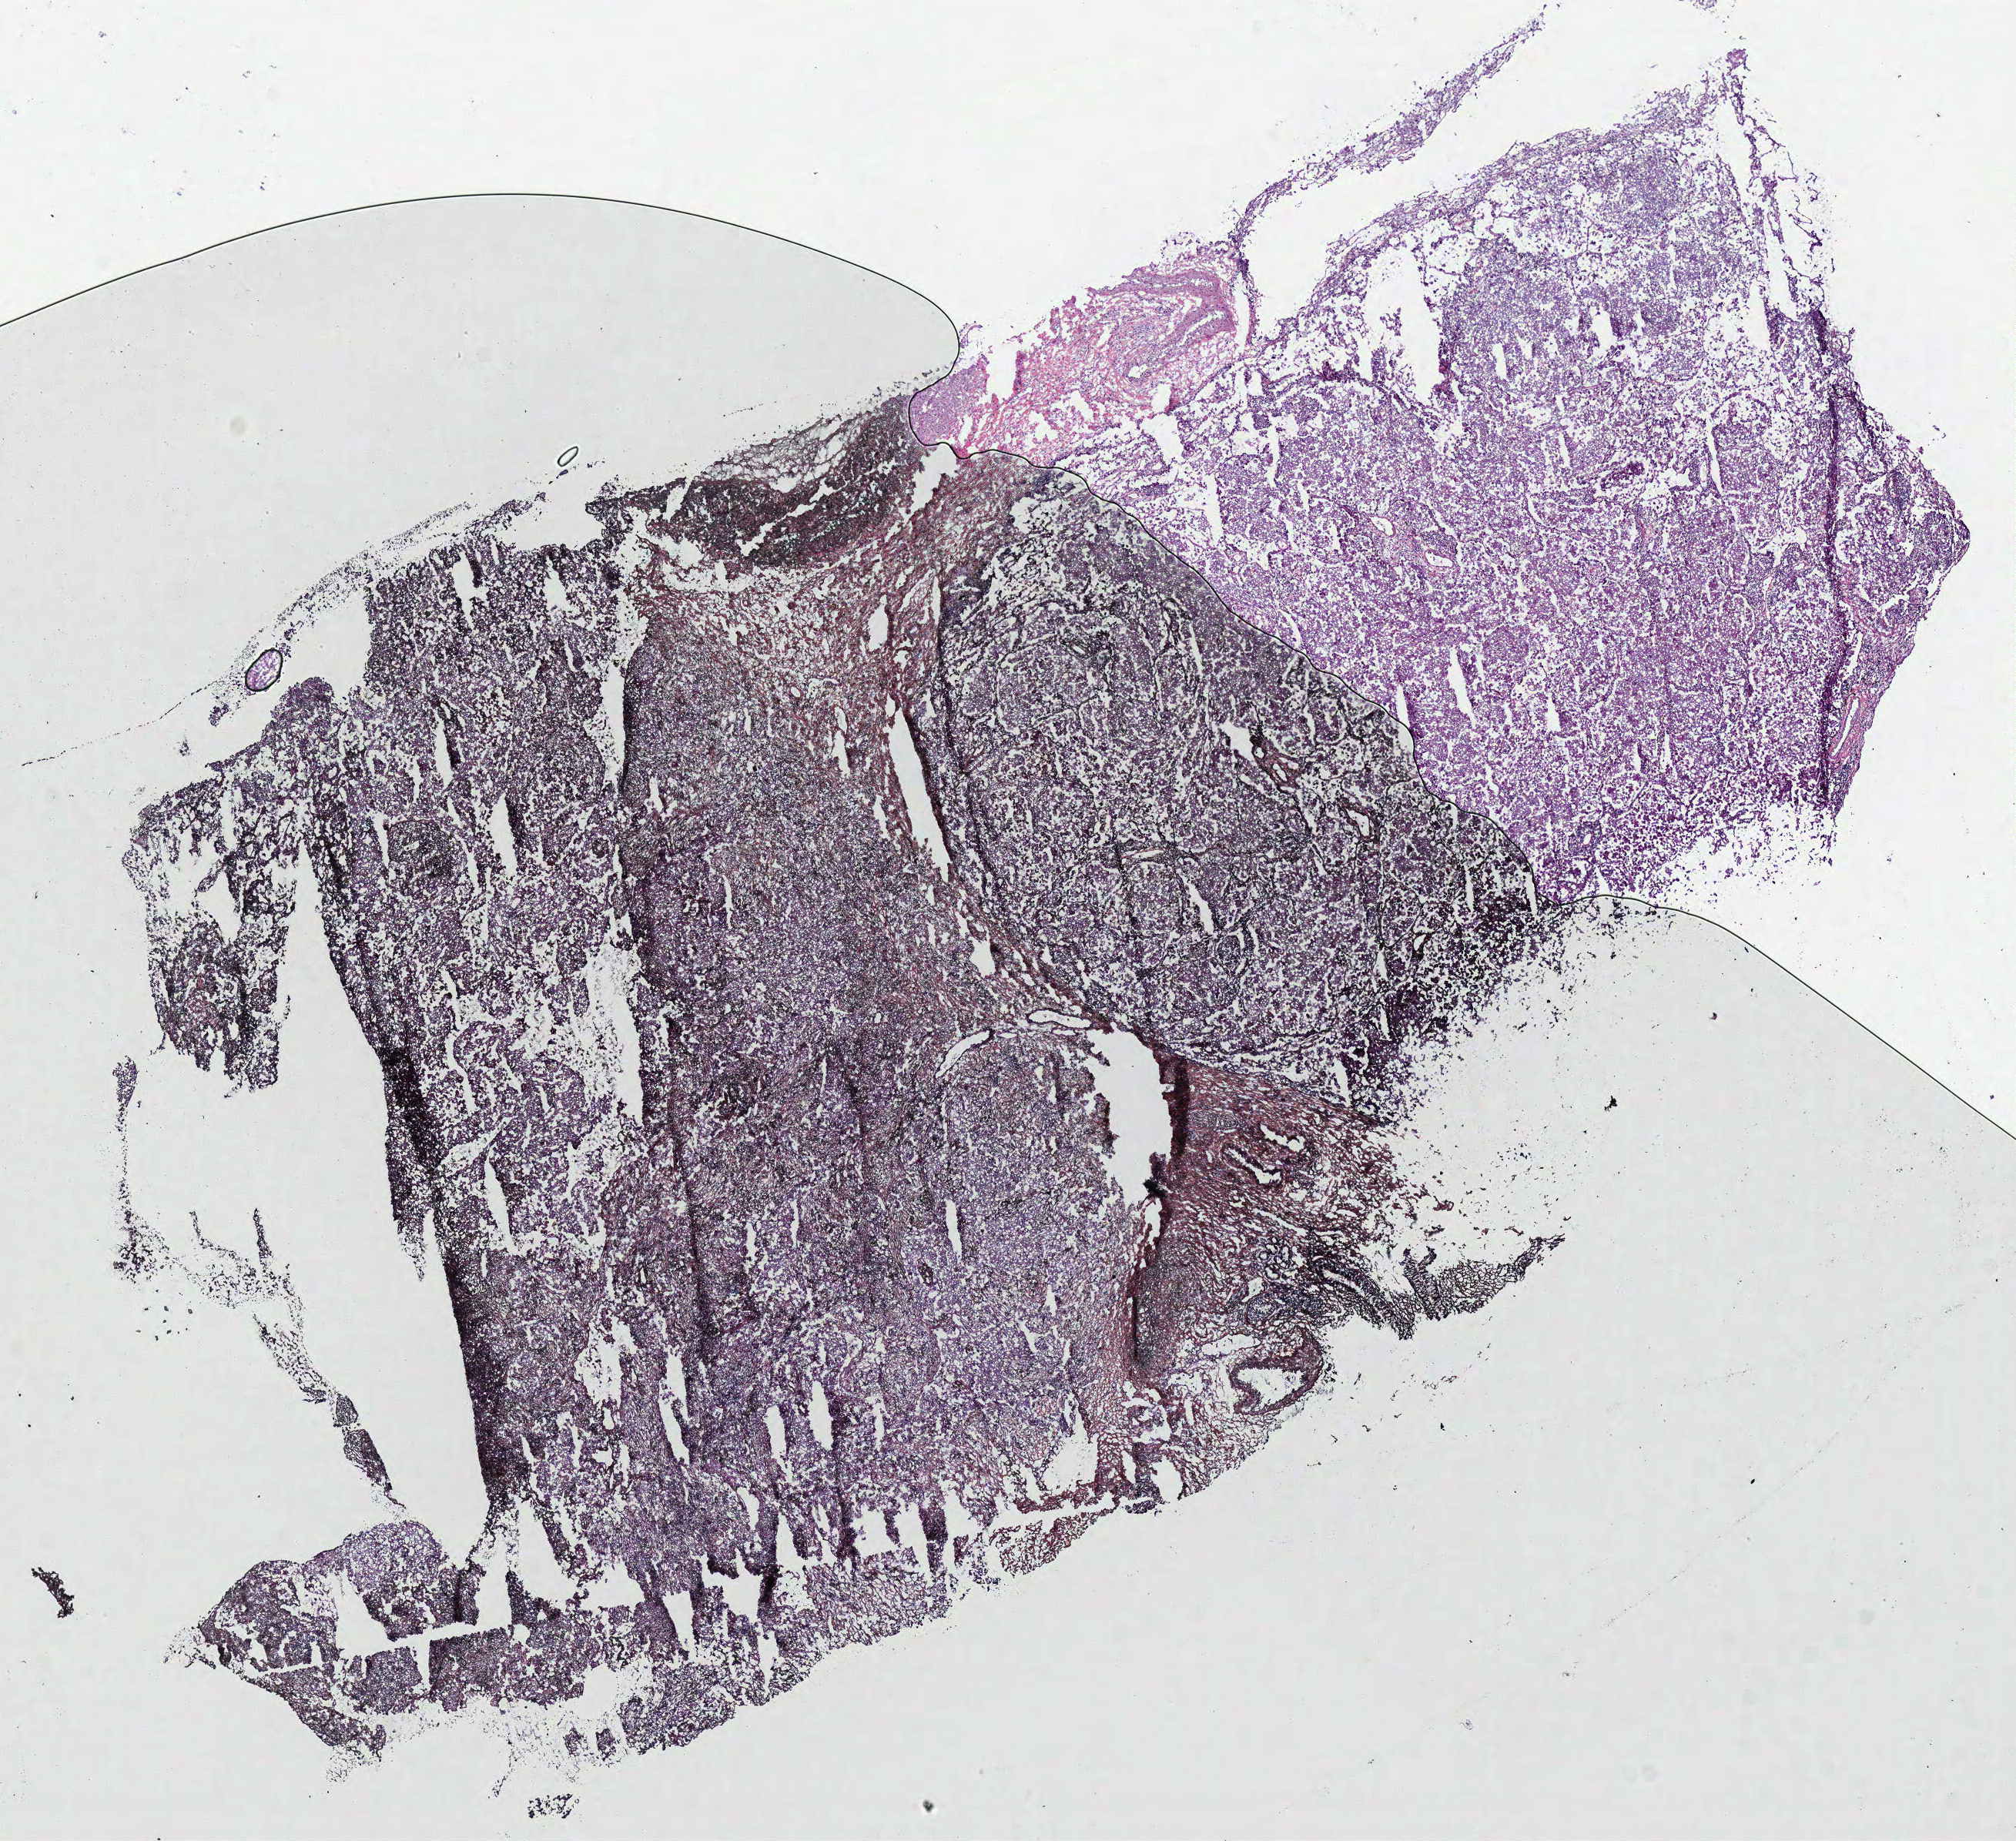
Whole-slide histology image, Hematoxylin and eosin (H&E) stained, whole scanned area (about 10.3 x 9.4 mm, slide scanned at 40x) shown as a low-resolution overview, frozen section from the top of the tissue portion, primary tumour sample from the lung. Male, age 82 years at initial diagnosis. Composition of this section per pathologist review: tumour cells 90%, tumour nuclei 80%, normal cells 0%, stromal cells 10%, necrosis 0%.
• histologic diagnosis: Papillary adenocarcinoma, NOS (upper lobe, lung)
• AJCC pathologic stage: IIIA (7th edition)
• laterality: left